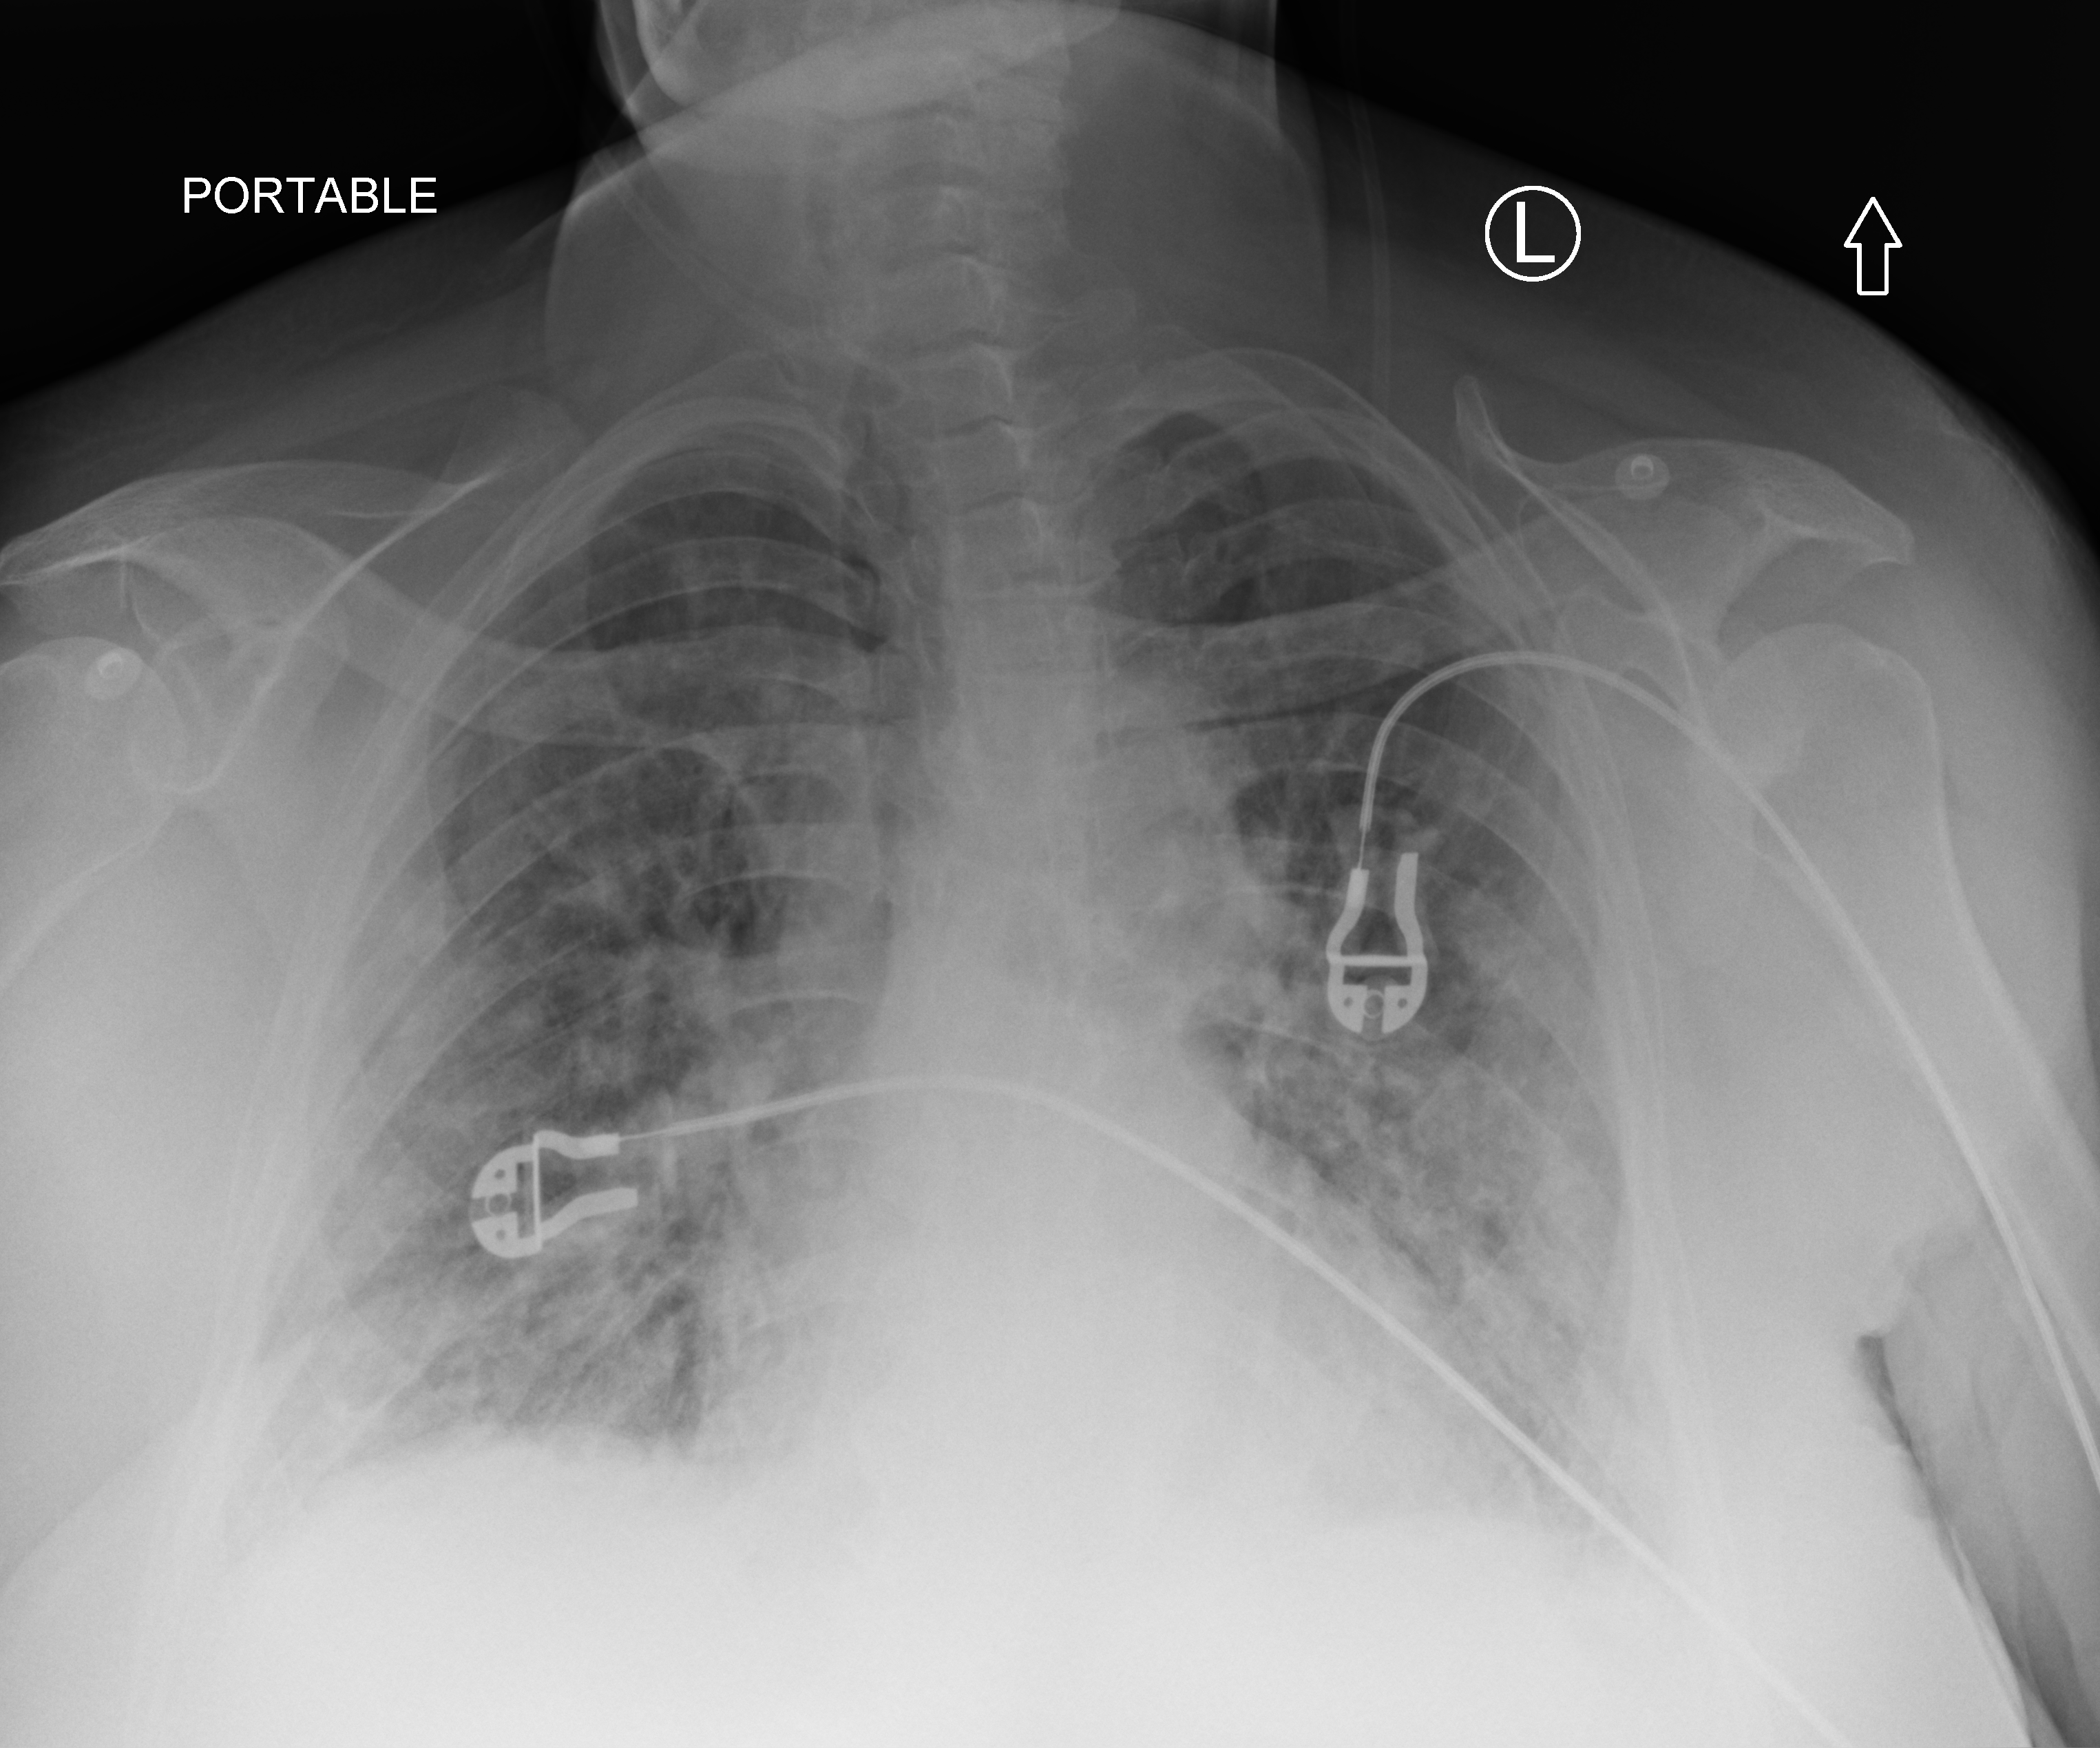
Portable chest radiograph. Patient hospitalised with COVID-19; female, aged 60–74 years.
Admission-level facts for this patient (not findings on this image; timing relative to this image not recorded):
- mechanically ventilated during this hospital stay: no
- chronic kidney disease (admission record): no